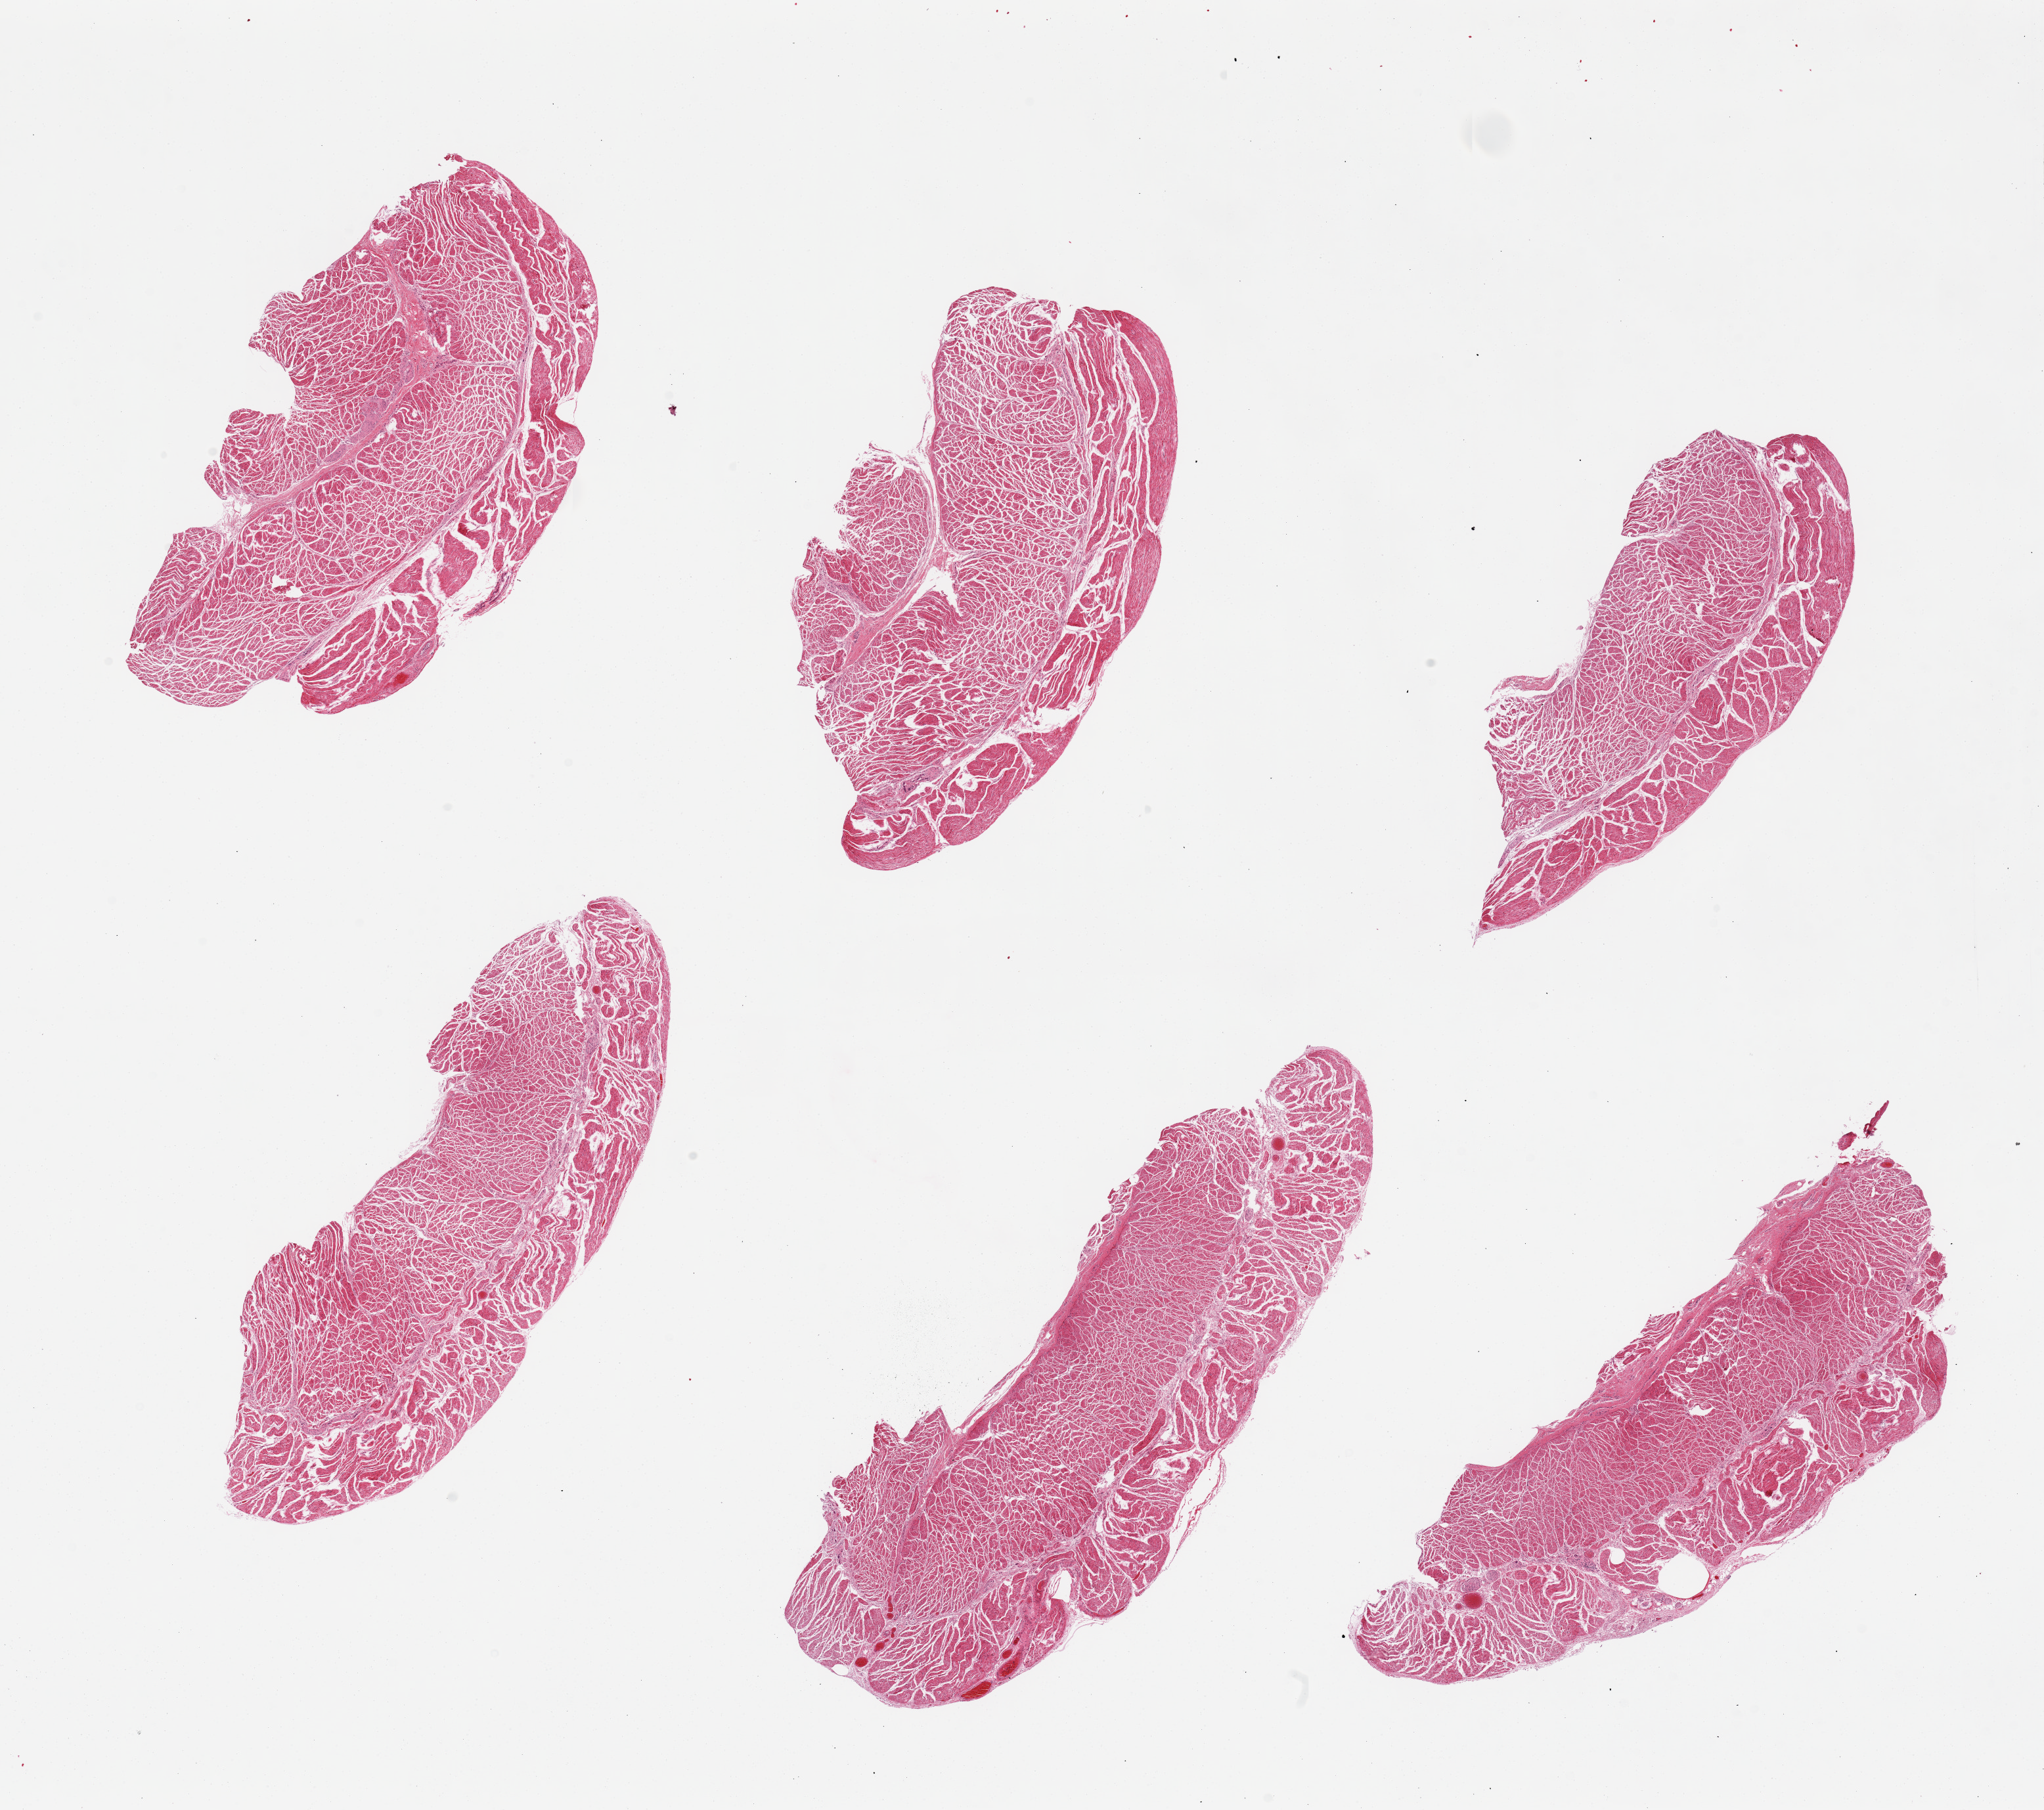
Whole-slide image, hematoxylin and eosin (H&E) stain, a low-resolution overview of the entire scanned area, about 24.6 x 21.8 mm, PAXgene-fixed, paraffin-embedded tissue, sampled site (target tissue): esophageal muscle, donor tissue sample. Female donor.
Review note (as recorded): 6 pieces; well dissected muscle.